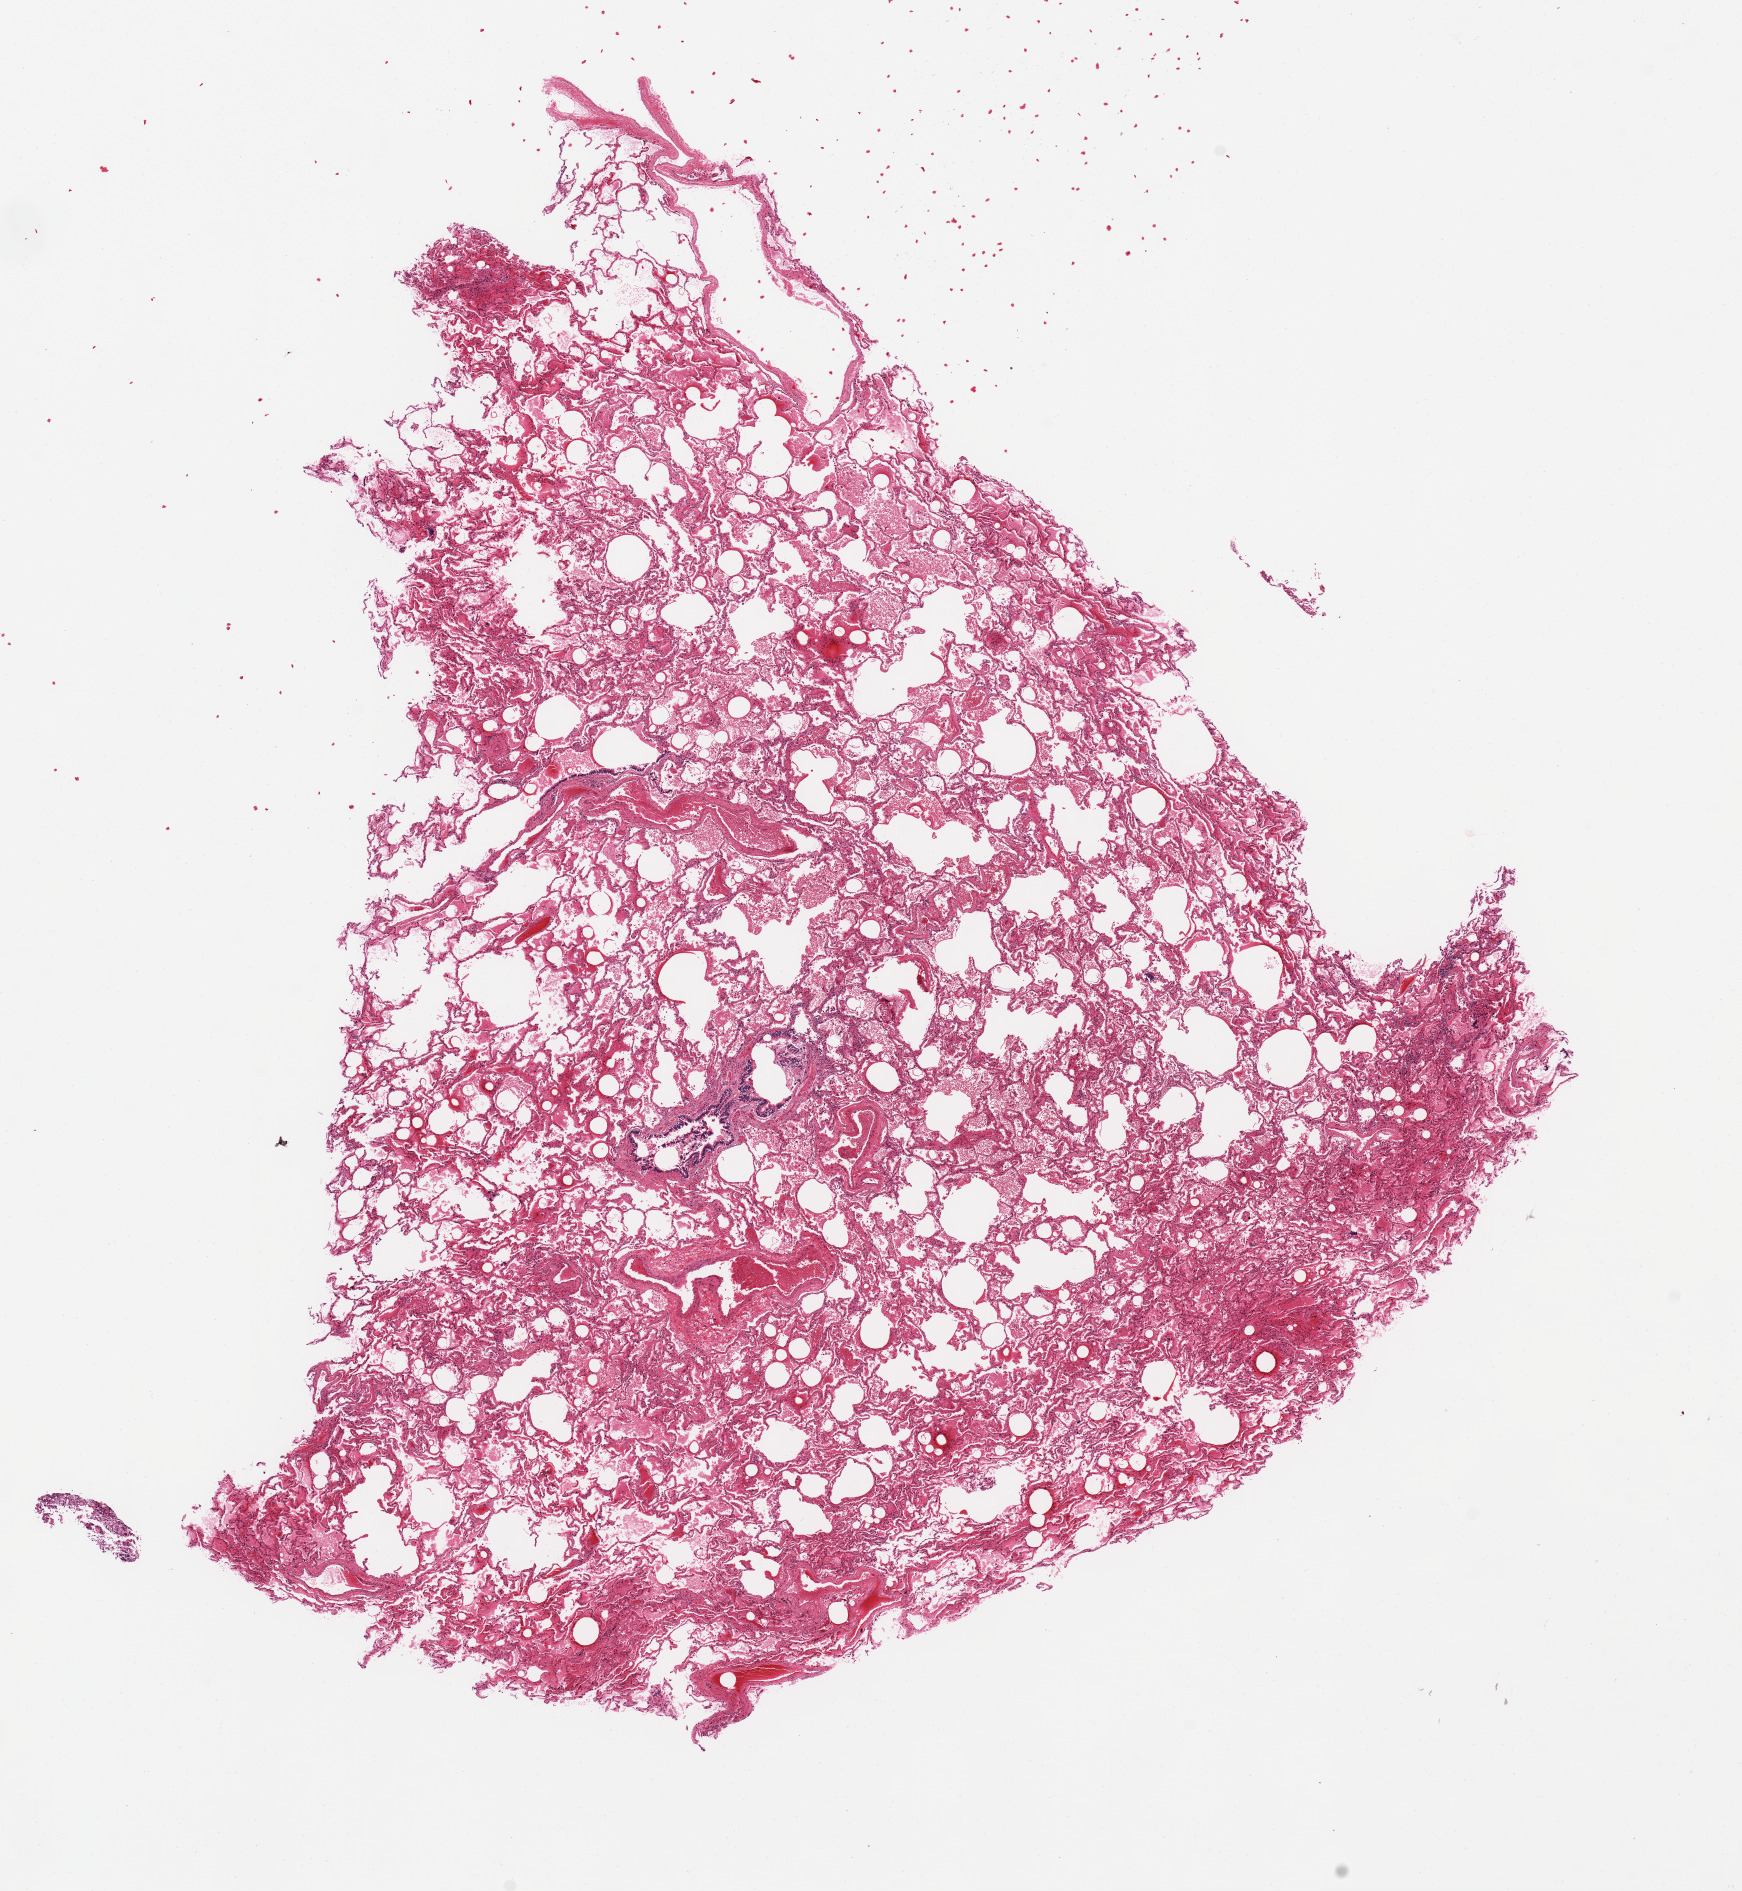
Whole-slide image, haematoxylin and eosin stain — a low-resolution overview of the entire scanned area, about 13.8 x 15.0 mm; PAXgene-fixed paraffin-embedded (PFPE) section; sampled site (target tissue): lung; donor tissue sample. Female donor.
- pathologist's review note for this sample: Alveolar exudates. 10x10mm